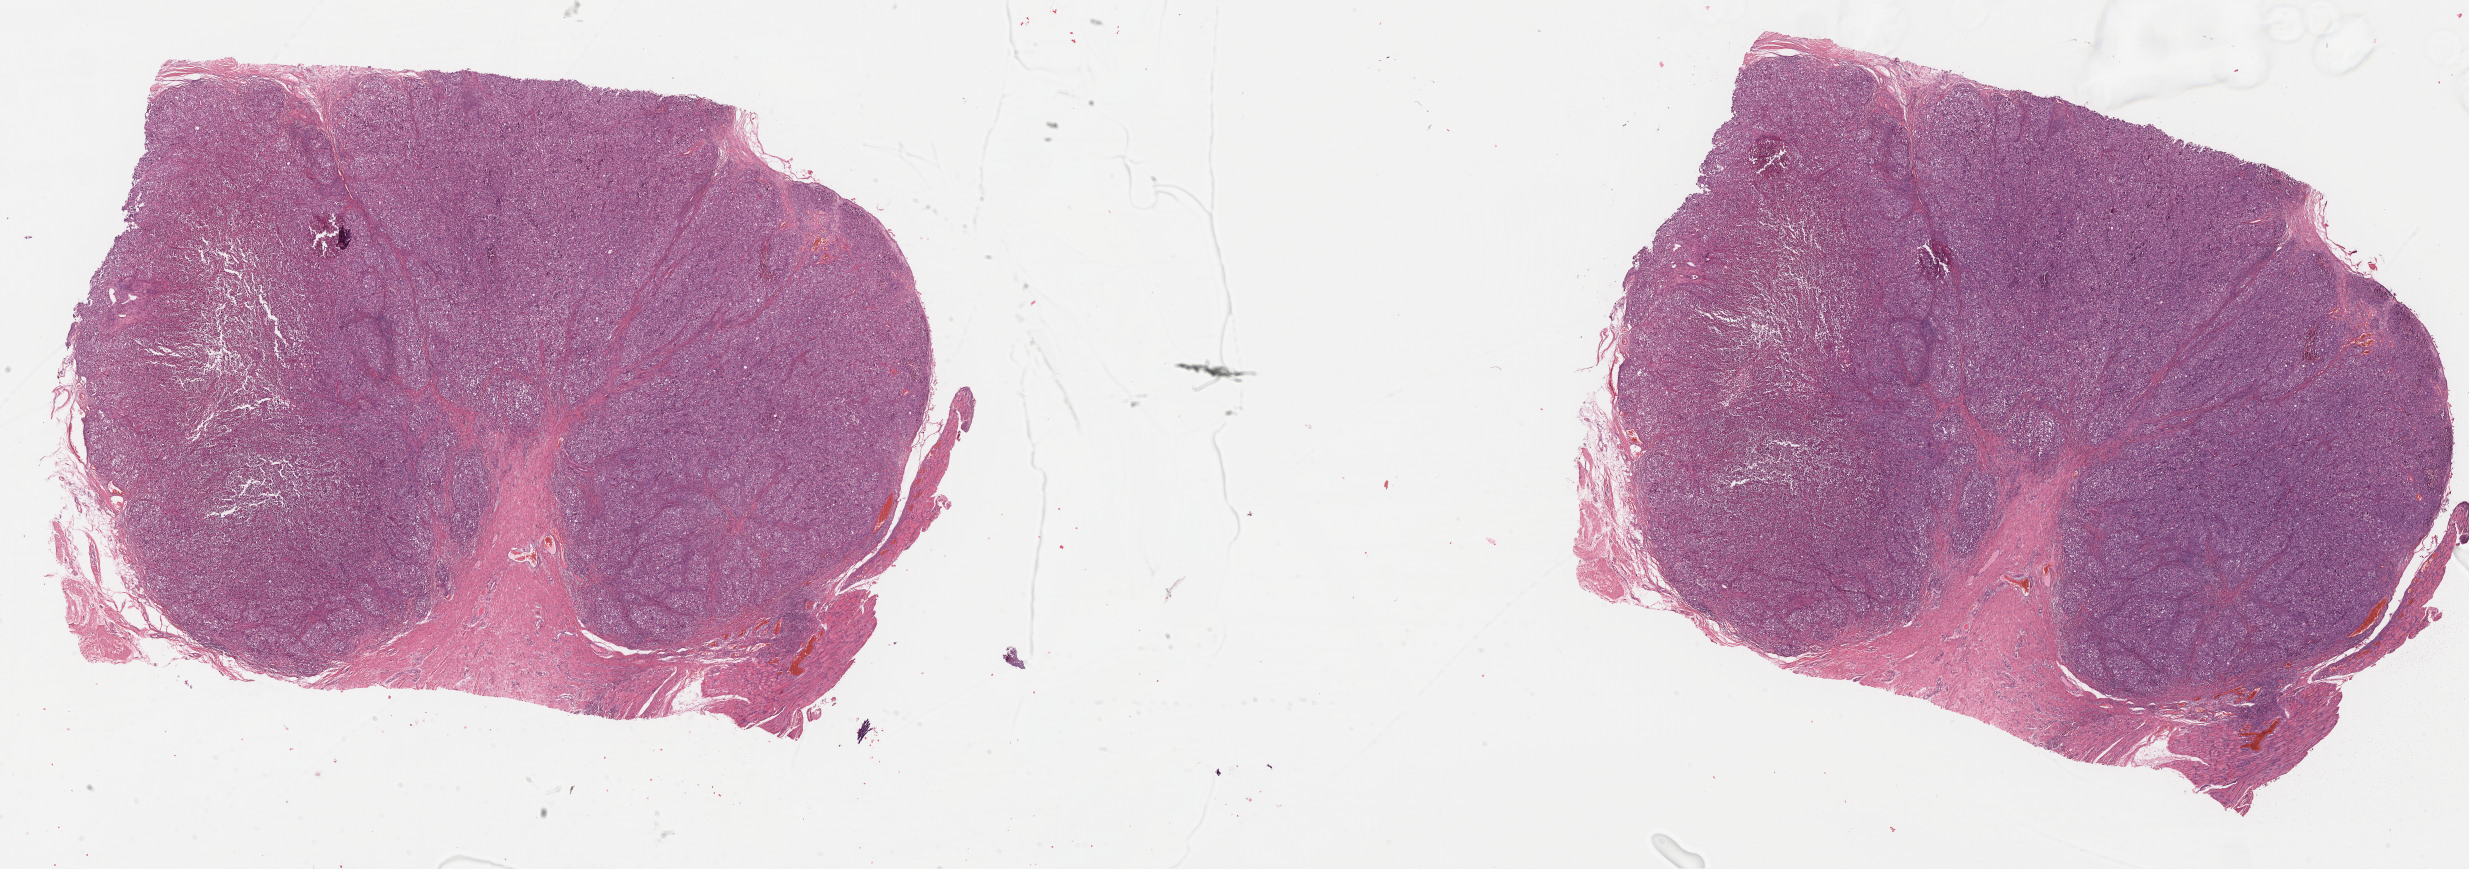
H&E-stained whole-slide image, a low-resolution overview of the entire scanned area, about 38.8 x 13.7 mm, formalin-fixed paraffin-embedded (FFPE) diagnostic section, metastatic tumour sample, sampled site: lymph node. Male patient; age at initial diagnosis 74 years.
This section: metastatic tumour tissue. Patient diagnosis: Malignant melanoma, NOS.